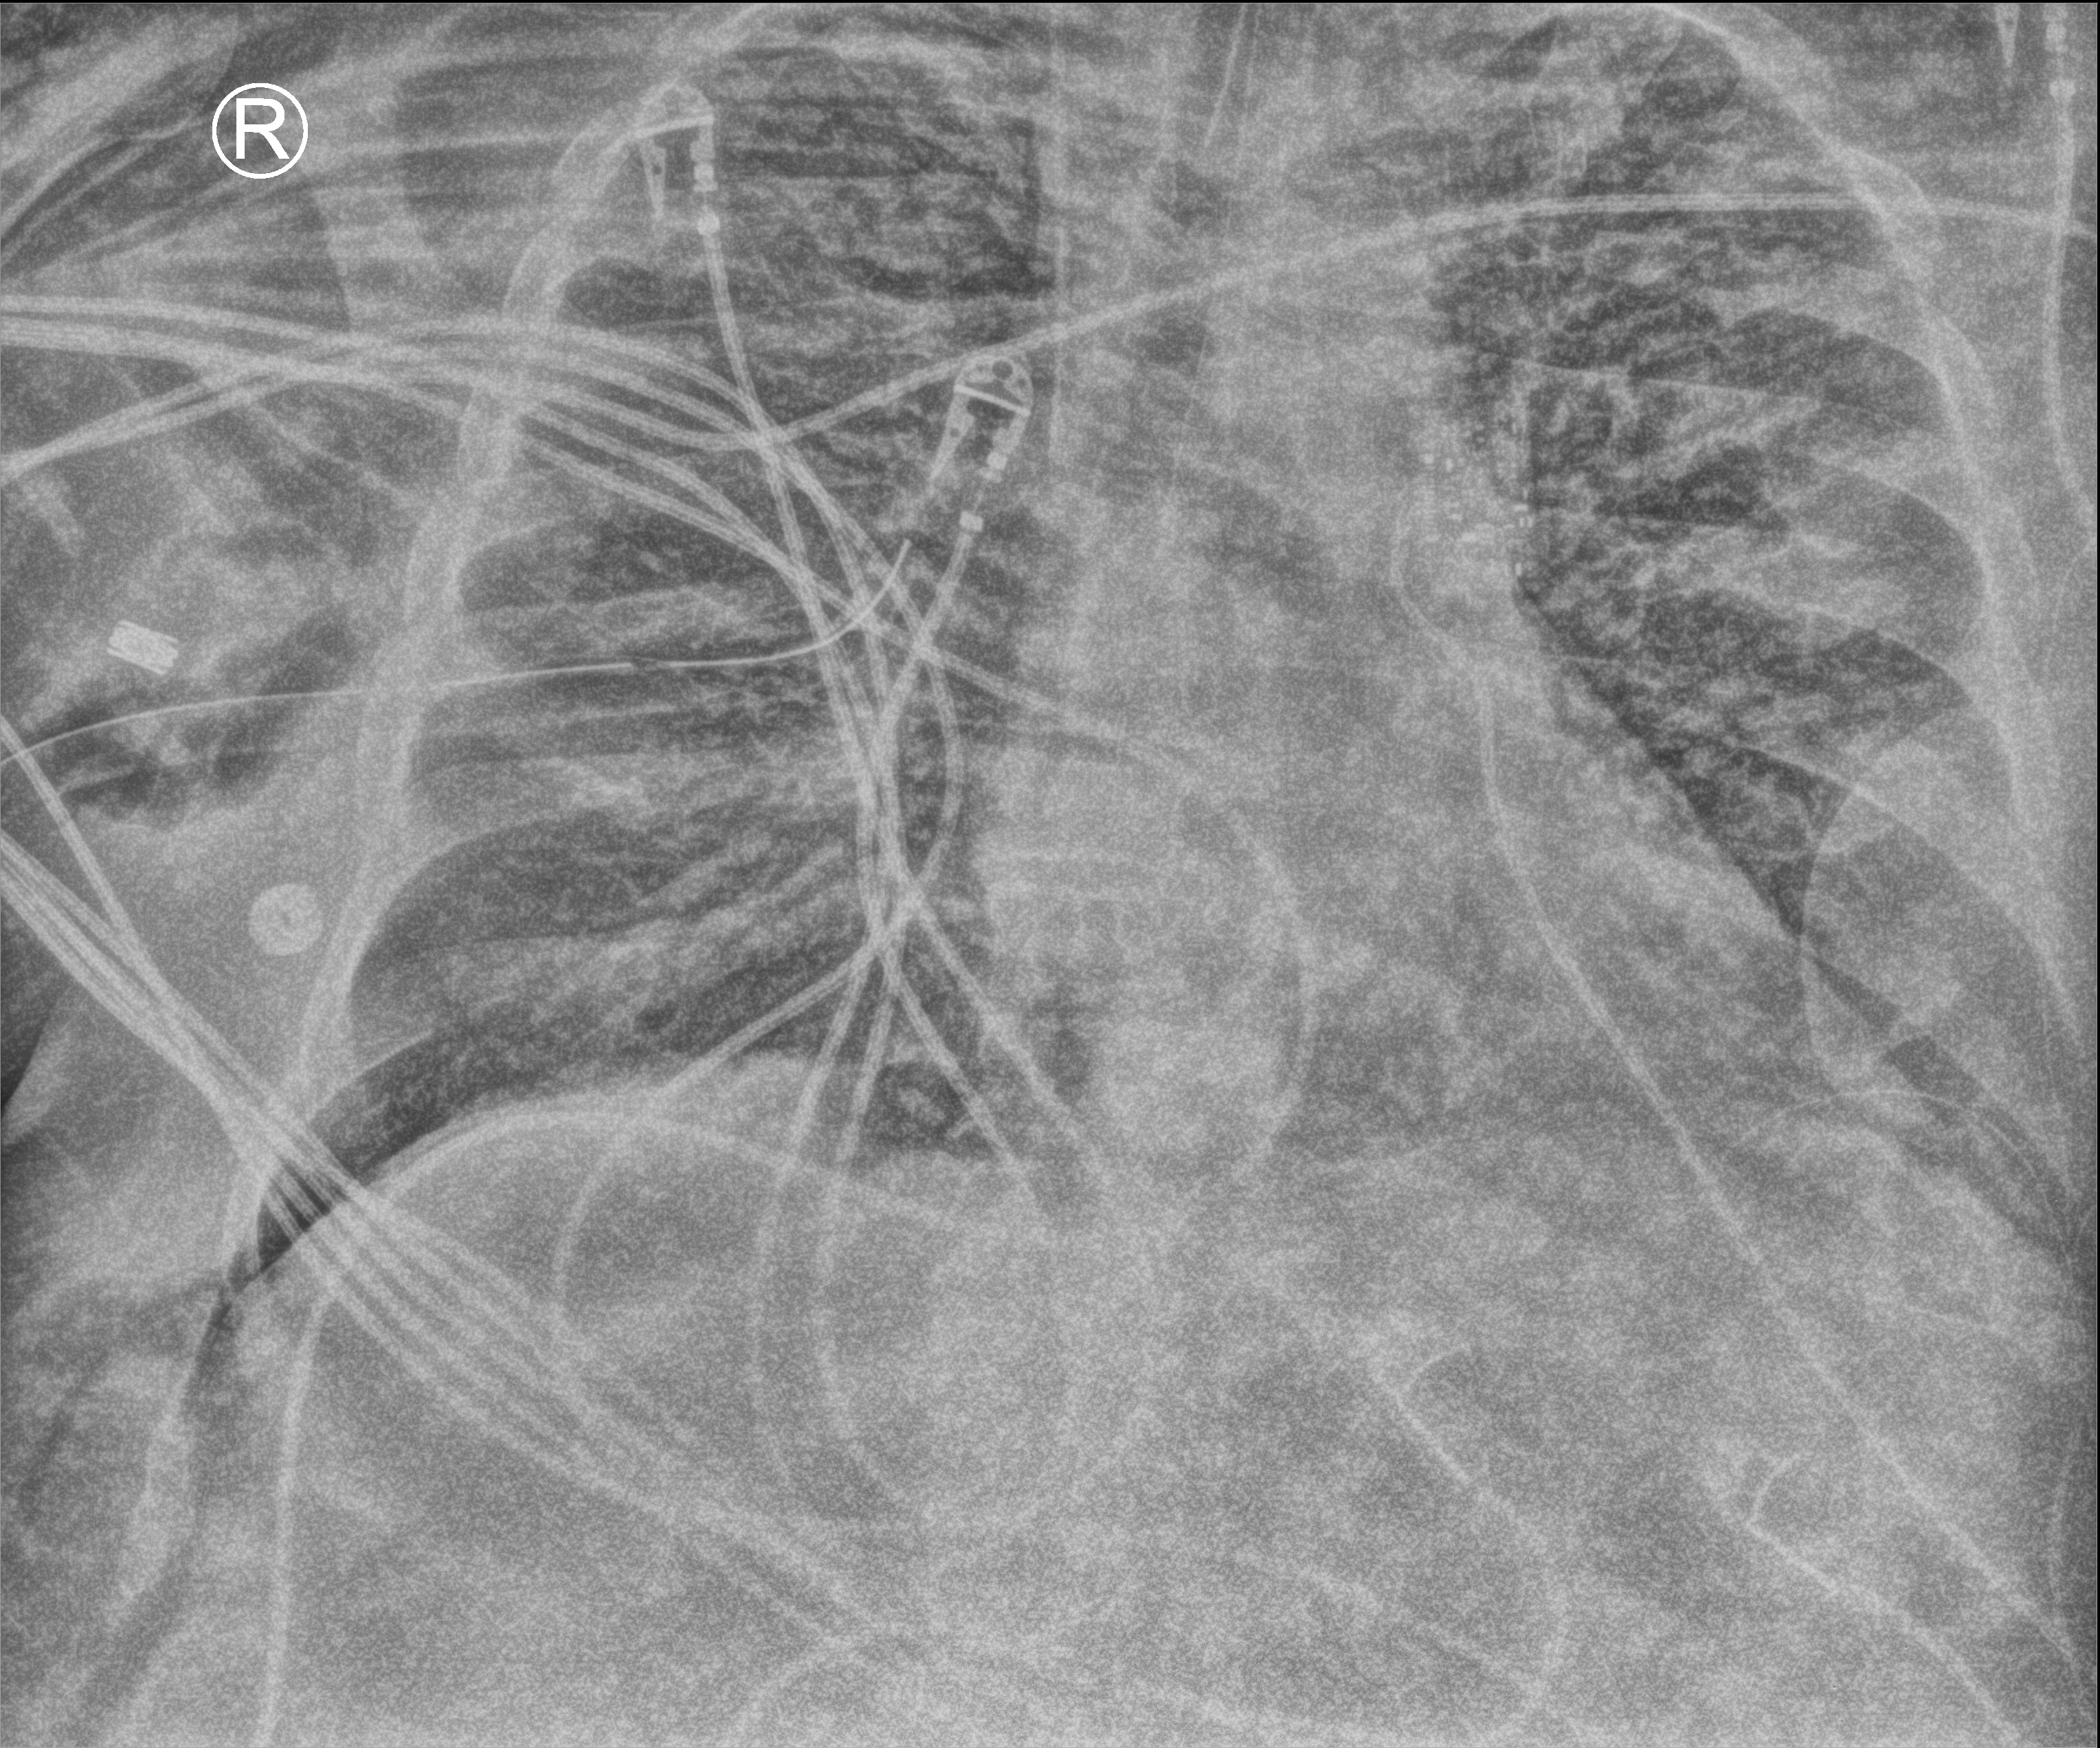
Chest X-ray (portable); anteroposterior (AP) projection. Adult patient hospitalised with COVID-19, age 18–59 years.
Admission-level facts for this patient (not findings on this image; timing relative to this image not recorded): admitted to intensive care during this hospital stay: yes.